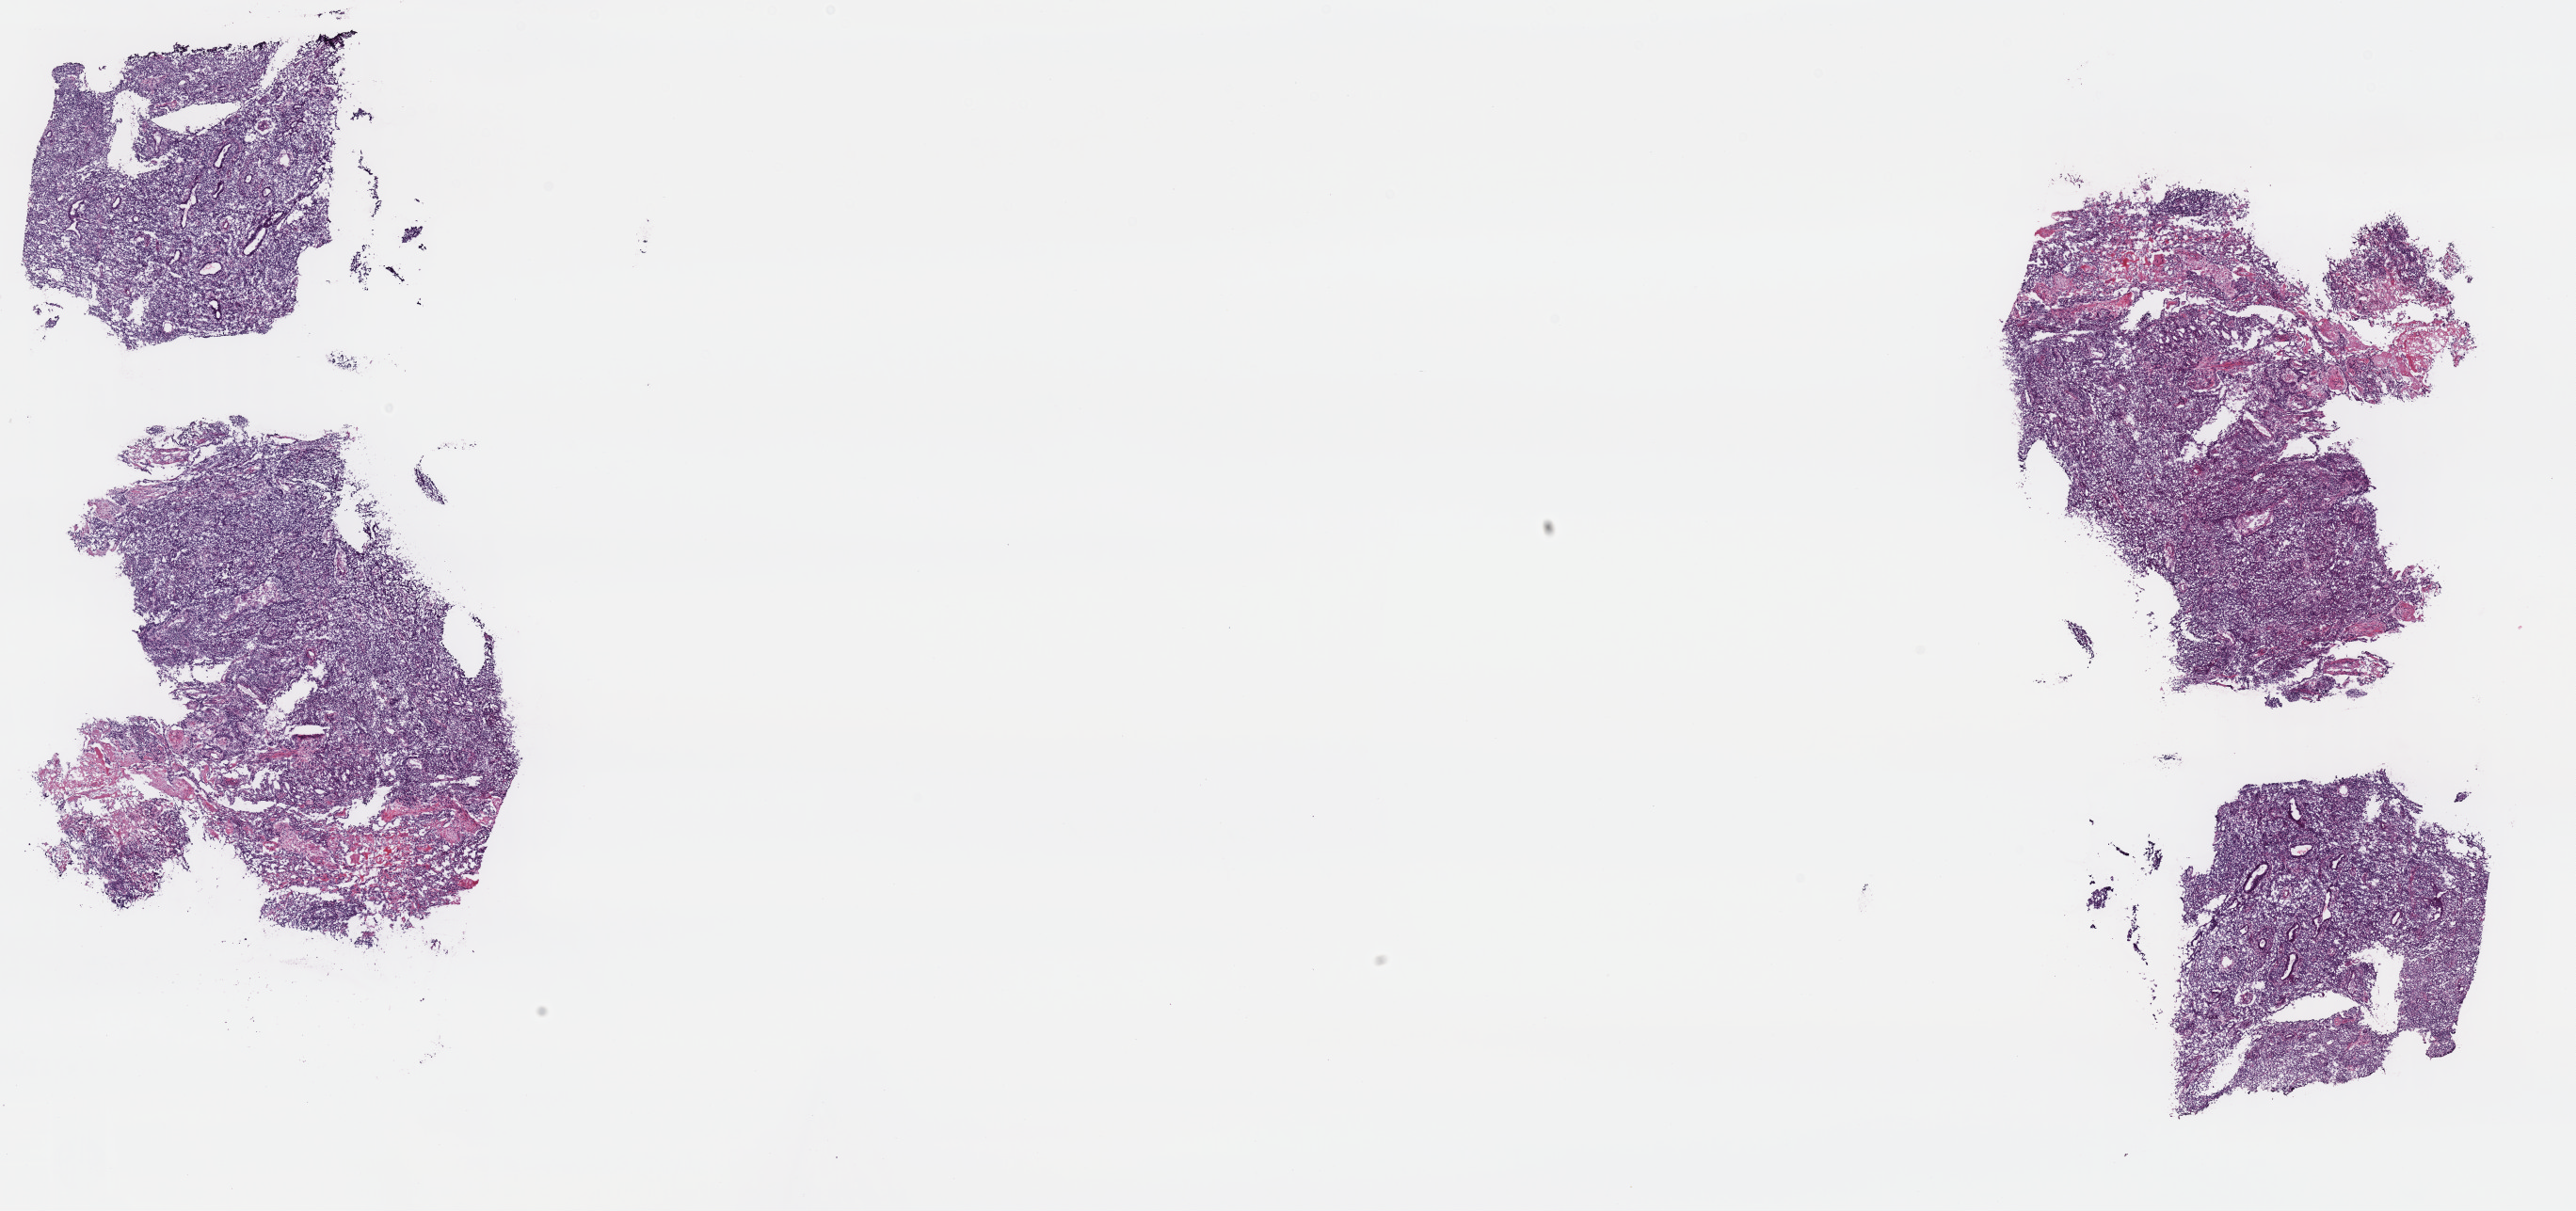
Whole-slide histology image, H&E — whole scanned area (about 21.6 x 10.2 mm, slide scanned at 40x) shown as a low-resolution overview. Frozen section from the top of the tissue portion. Uterus, primary tumour sample. Female, age 68 years at initial diagnosis.
Histologic diagnosis: Endometrioid adenocarcinoma, NOS (endometrium).